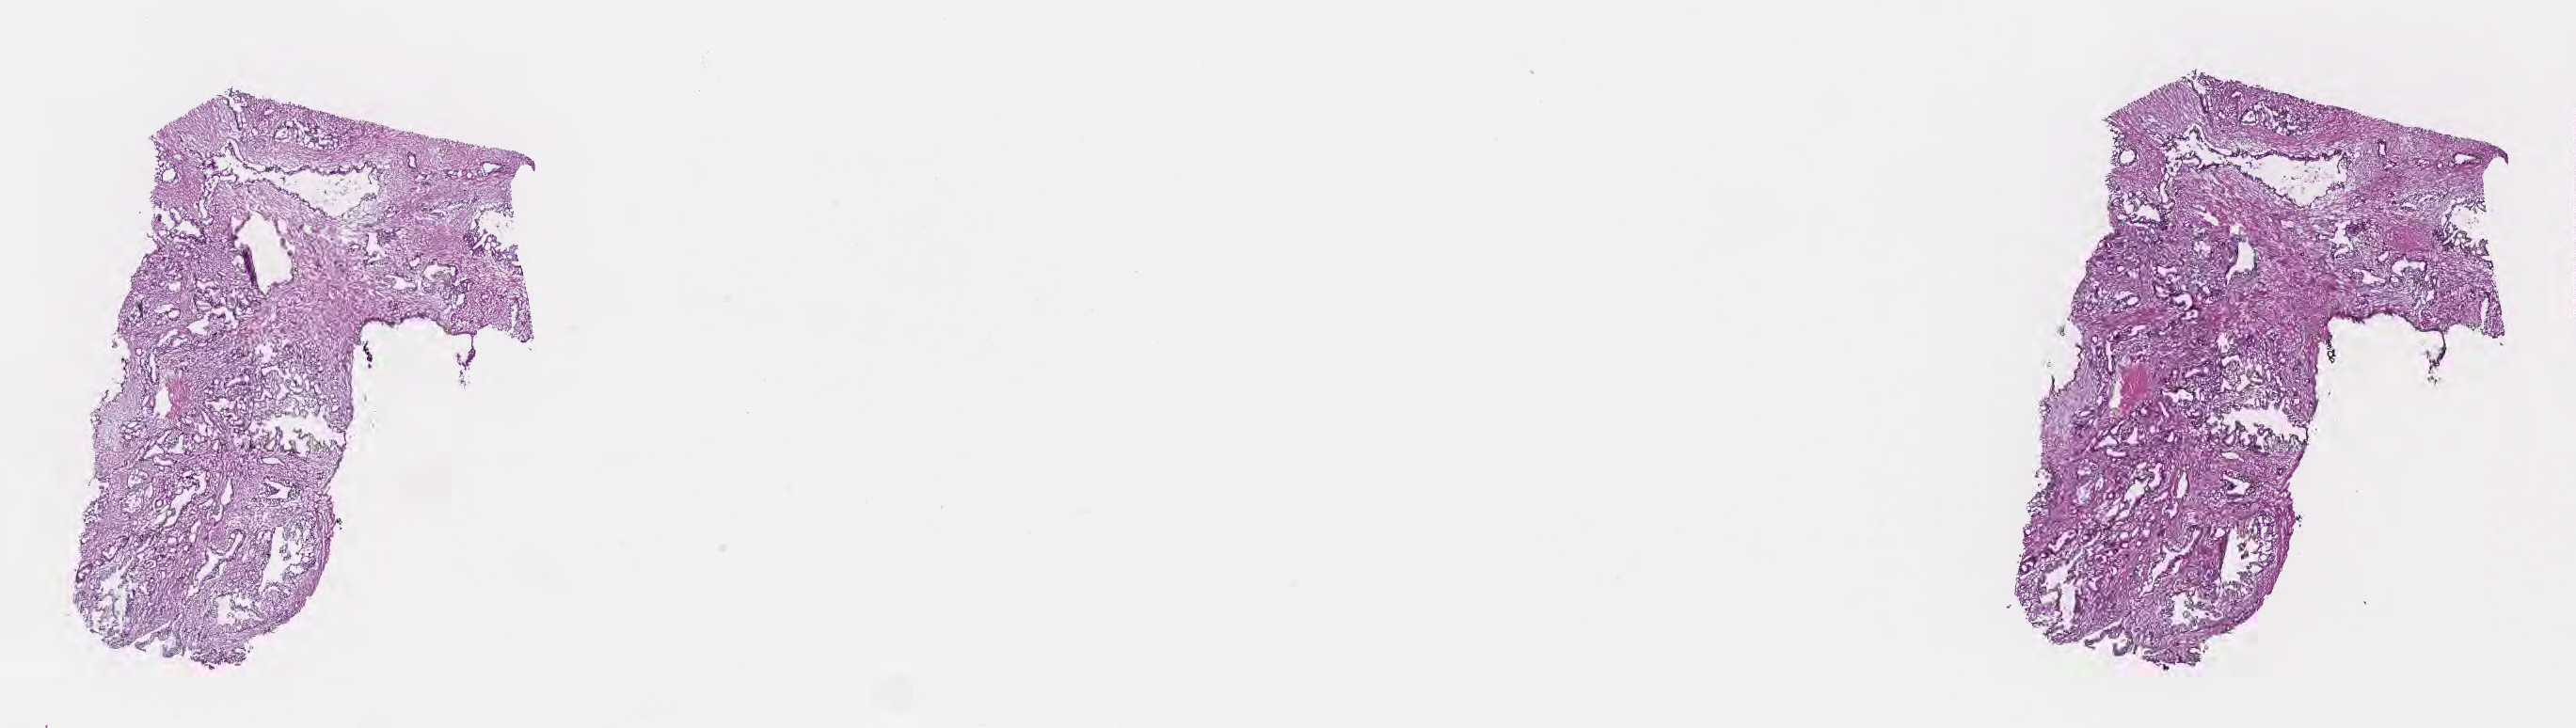
Whole-slide image, haematoxylin and eosin stain — whole scanned area (about 22.1 x 6.3 mm) shown as a low-resolution overview. Frozen section. Primary tumor. Site: tail of pancreas. Female, age 74 years at initial diagnosis. Slide review estimates, as recorded: tumor cells 50%, tumor nuclei 50%.
Diagnosis: Infiltrating duct carcinoma, NOS.